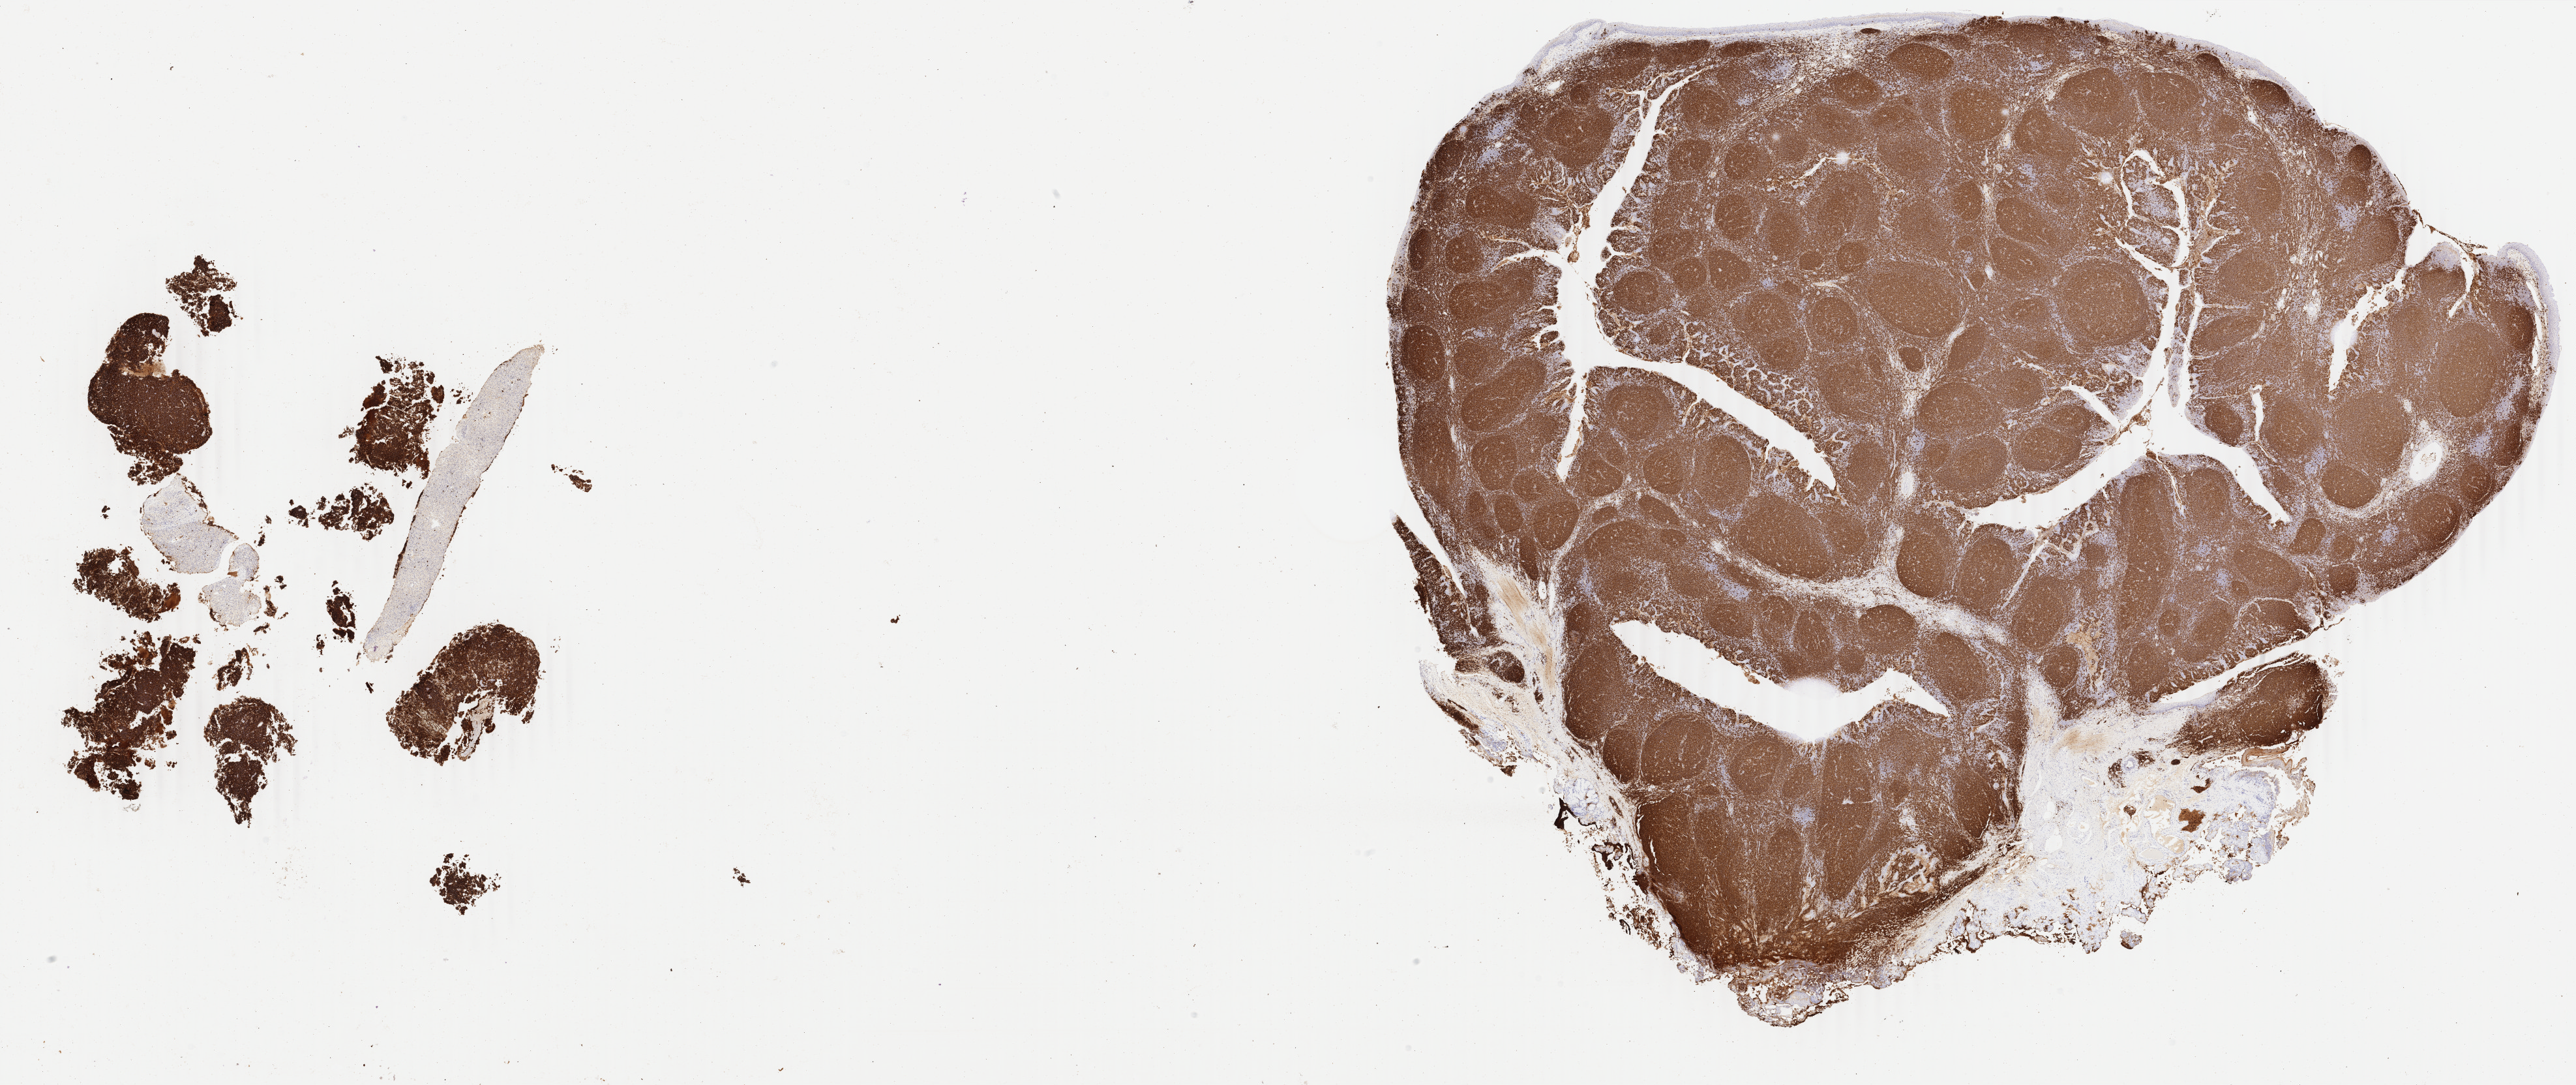
IHC for CD20, whole-slide image — shown as a low-resolution overview of the whole scanned area (about 31.4 x 13.2 mm), specimen: tumor tissue, anatomic site: liver. Male patient; age at initial diagnosis 5 years.
Histologic diagnosis: Burkitt lymphoma, NOS.